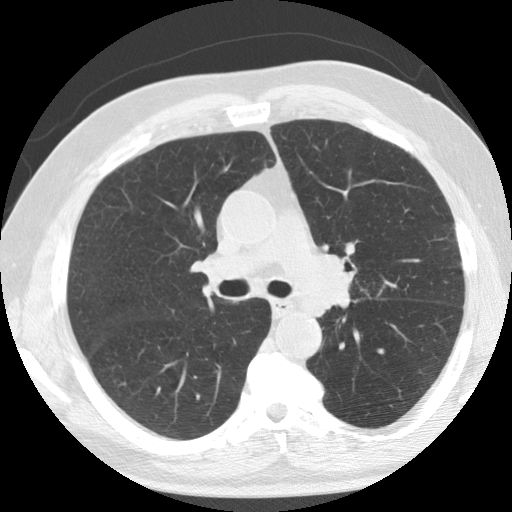
Low-dose screening chest CT, one axial slice. Slice 83 of 133 in the series (ordered by position). Lung window (W 1500 / L -600 HU). 512 × 512 image matrix.
Structures marked on this image (expert manual segmentation):
- lesion 1 (tumor, upper lobe of left lung): box from (x=311, y=255) to (x=353, y=314) px